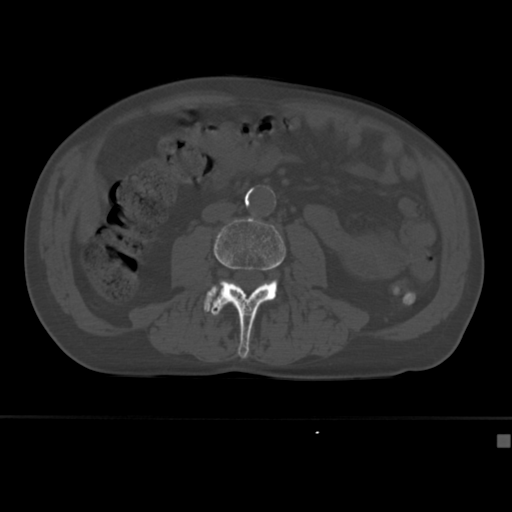
CT including the spine, one axial slice. Slice 124 of 430 in the series (ordered by position). Reconstruction kernel Br40s. Bone window (W 1800 / L 400 HU). 1.5 mm slice thickness. 512 × 512 image matrix, field of view 337 × 337 mm. Patient: male, 64 years. Case-level facts recorded for this patient, not image findings: primary cancer: uterus.
Annotated regions visible in this slice (semi-automatic segmentation, software-assisted and operator-edited):
- L3 vertebra: box from (x=211, y=217) to (x=286, y=359) px
- L4 vertebra: (x=204, y=286)–(x=218, y=312)